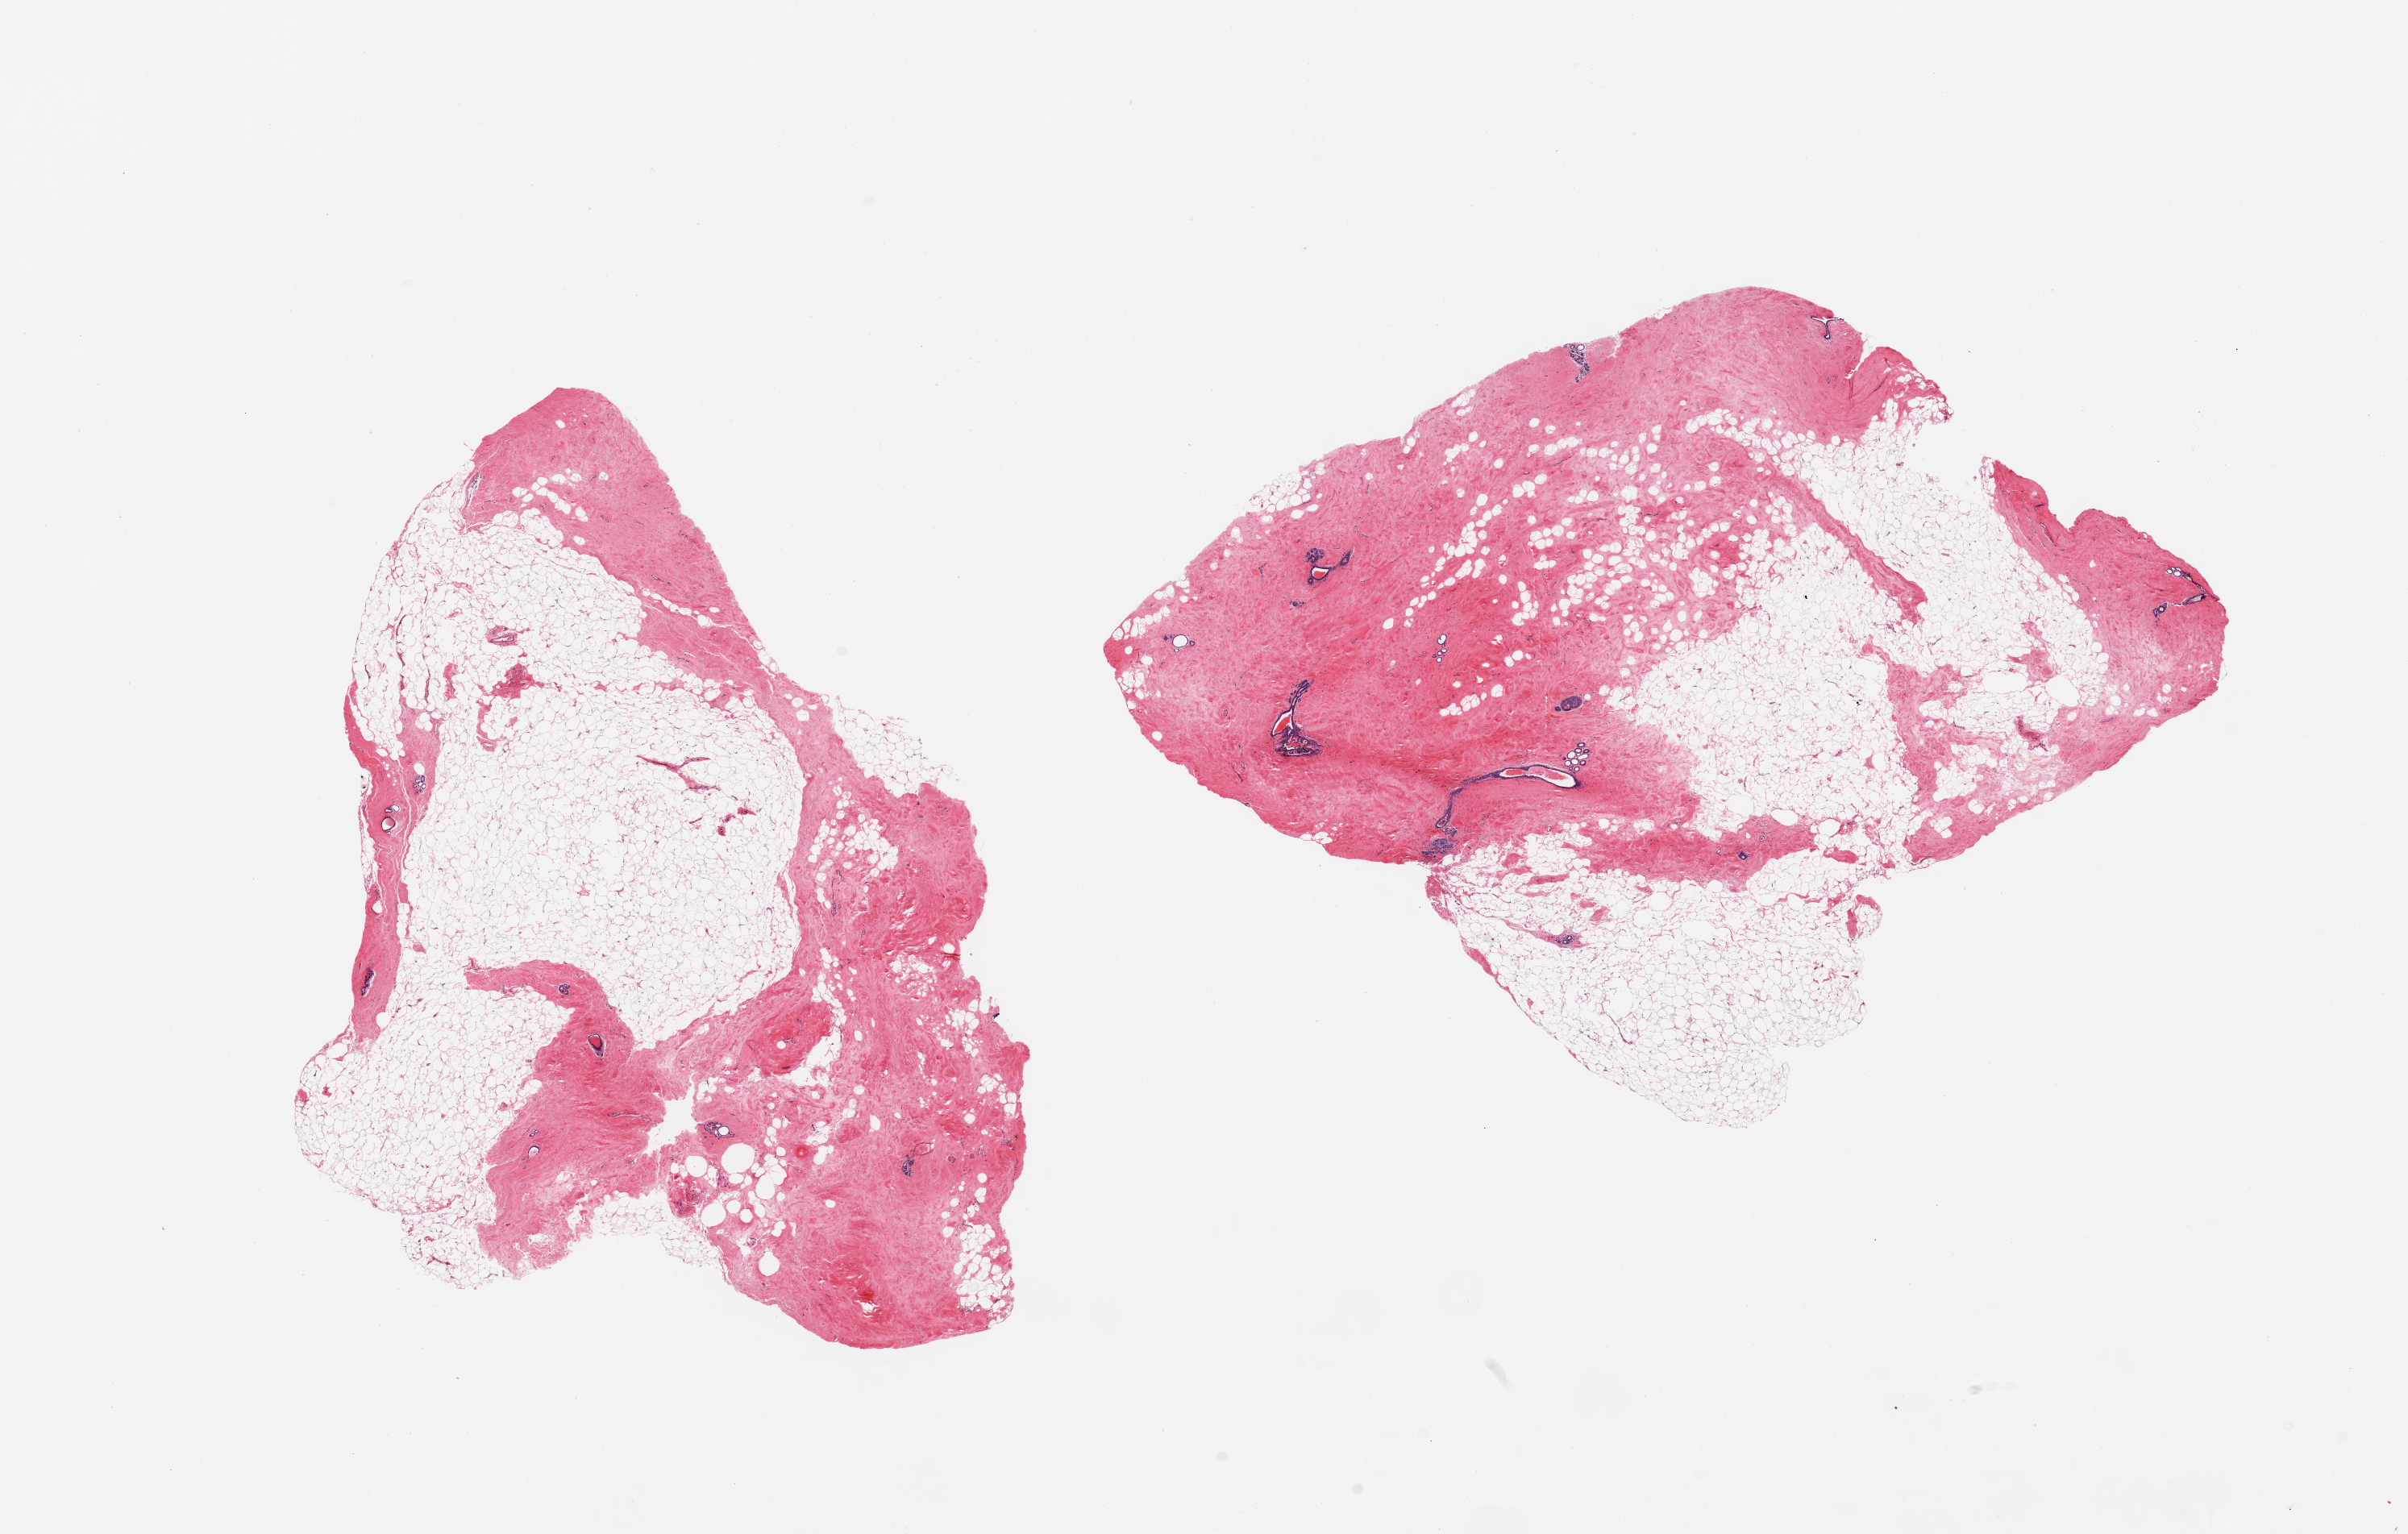
Digitized hematoxylin and eosin (H&E)-stained section, a low-resolution overview of the entire scanned area, about 23.6 x 15.1 mm (from a 20x scan); PAXgene-fixed, paraffin-embedded tissue; sampled site (target tissue): breast; tissue donor sample.
* pathologist's review note for this sample: 2 pieces, 50-60% fat, rest is dense fibrous stroma and ductal/lobular elements